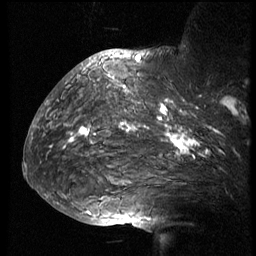
Breast MRI (dynamic contrast-enhanced), one sagittal slice; slice 50 of 74 in the series (ordered by position); 3 images stored at this slice position (order not interpretable as contrast timing); 1.5 T; TE 4.2 ms, TR 8.9 ms; 2.5 mm slice thickness; 256 × 256 image matrix, field of view 200 × 200 mm. Patient: female, 57 years. Case-level facts recorded for this patient, not image findings: setting: breast cancer imaged before/during neoadjuvant chemotherapy; receptor status: HER2-positive.
Outlined on this slice (semi-automatic segmentation, software-assisted and operator-edited):
- analysis volume of interest (the breast-tissue region the enhancement analysis was run in; not a lesion): box from (x=51, y=67) to (x=248, y=173) px
- tumour enhancement mask (voxels above the 140 % enhancement threshold inside the analysis volume of interest): (x=70, y=75)–(x=239, y=156)